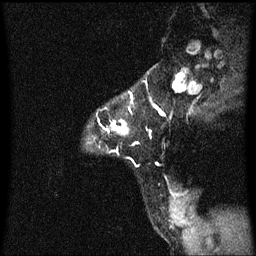
Breast MRI (dynamic contrast-enhanced), one sagittal slice; position 49 of 60 along the scan axis; dynamic contrast-enhanced series, image 2 of 3 at this slice position (ordered by acquisition); 1.5 T; TE 4.2 ms, TR 8.4 ms; 256 × 256 image matrix, field of view 200 × 200 mm. Female patient, age 32 years.
Outlined on this slice (semi-automatically segmented with operator editing):
- analysis volume of interest (the breast-tissue region the enhancement analysis was run in; not a lesion): bounding box [x1, y1, x2, y2] px = [98, 92, 130, 135]
- tumour enhancement mask (voxels above the 70 % enhancement threshold inside the analysis volume of interest): [113, 120, 128, 135]